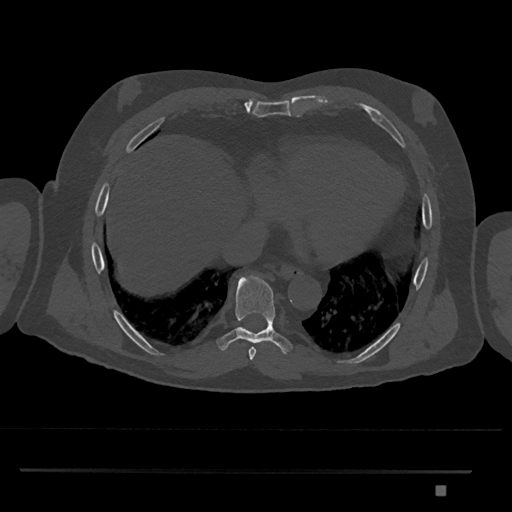
CT including the spine, one axial slice. Slice 1114 of 1134 in the series (ordered by position). Reconstruction kernel Br40s/3. 120 kVp. Bone window (W 1800 / L 400 HU). 0.5 mm slice thickness. 512 × 512 image matrix, field of view 429 × 429 mm. Patient: male, 65 years. From the clinical record (not read from this slice): primary cancer: prostate.
Structures marked on this image (semi-automatic segmentation, software-assisted and operator-edited):
- T8 vertebra: bounding box (x1, y1, x2, y2) in pixels: (216, 275, 293, 354)